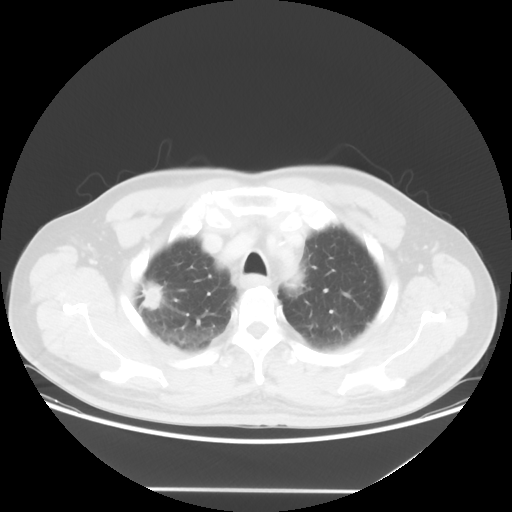
Chest CT, one axial slice; slice 44 of 54 in the series (ordered by position); reconstruction kernel STANDARD; 120 kVp; lung window (W 1500 / L -600 HU); 5 mm slice thickness; 512 × 512 image matrix, field of view 416 × 416 mm. Patient: male, 65 years. Case-level facts recorded for this patient, not image findings: clinical TNM (as recorded): T1c N1 M0.
Outlined on this slice (rectangle marked by the reading radiologist):
- lung tumour (recorded histology: adenocarcinoma): bounding box <136,275,170,315> (left, top, right, bottom; pixels)